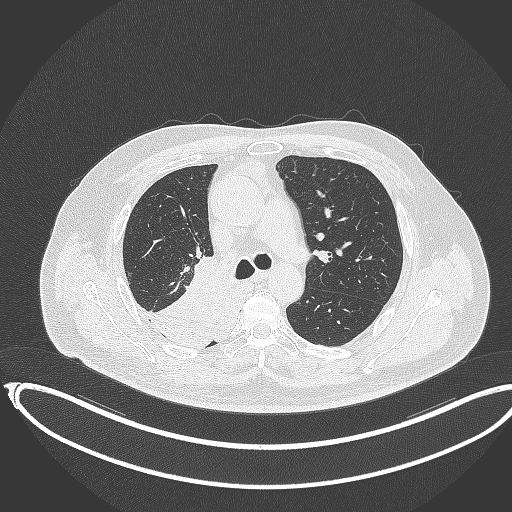
Chest CT, one axial slice; slice 236 of 403 in the series (ordered by position); reconstruction kernel B70f; 120 kVp; lung window (W 1500 / L -600 HU); 1 mm slice thickness; 512 × 512 image matrix, field of view 436 × 436 mm. Male patient, age 68 years. From the clinical record (not read from this slice): clinical TNM (as recorded): T2a N0 M0.
Structures marked on this image (bounding box drawn by a radiologist):
- lung tumour (recorded histology: adenocarcinoma): bounding box [x1, y1, x2, y2] px = [135, 255, 229, 350]